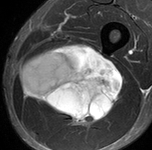
MRI of an extremity soft-tissue mass, one axial slice. Slice 56 of 90 in the series (ordered by position). STIR. MR volume resampled by the dataset authors to the PET/CT grid (not the native acquisition matrix). 3.27 mm slice thickness. 152 × 150 image matrix, field of view 148 × 146 mm. Male patient. From the clinical record (not read from this slice): histological type: undifferentiated pleomorphic liposarcoma; grade: high; site of the primary tumour: left thigh.
Outlined on this slice (expert contour drawn on MRI and transferred to this co-registered scan by the dataset authors):
- gross tumour volume including surrounding oedema: bounding box <20,44,124,127> (left, top, right, bottom; pixels)
- gross tumour volume (mass): <20,44,124,125>